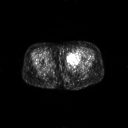
FDG PET of an extremity soft-tissue mass (from a PET/CT study), one axial slice; 3.27 mm slice thickness; 128 × 128 image matrix, field of view 700 × 700 mm. Female patient, age 47 years. From the clinical record (not read from this slice): histological type: myxofibrosarcoma; grade: intermediate; site of the primary tumour: left thigh.
Outlined on this slice (expert contour drawn on MRI and transferred to this co-registered scan by the dataset authors):
- gross tumour volume including surrounding oedema: box from (x=66, y=51) to (x=81, y=64) px
- gross tumour volume (mass): (x=67, y=52)–(x=81, y=64)